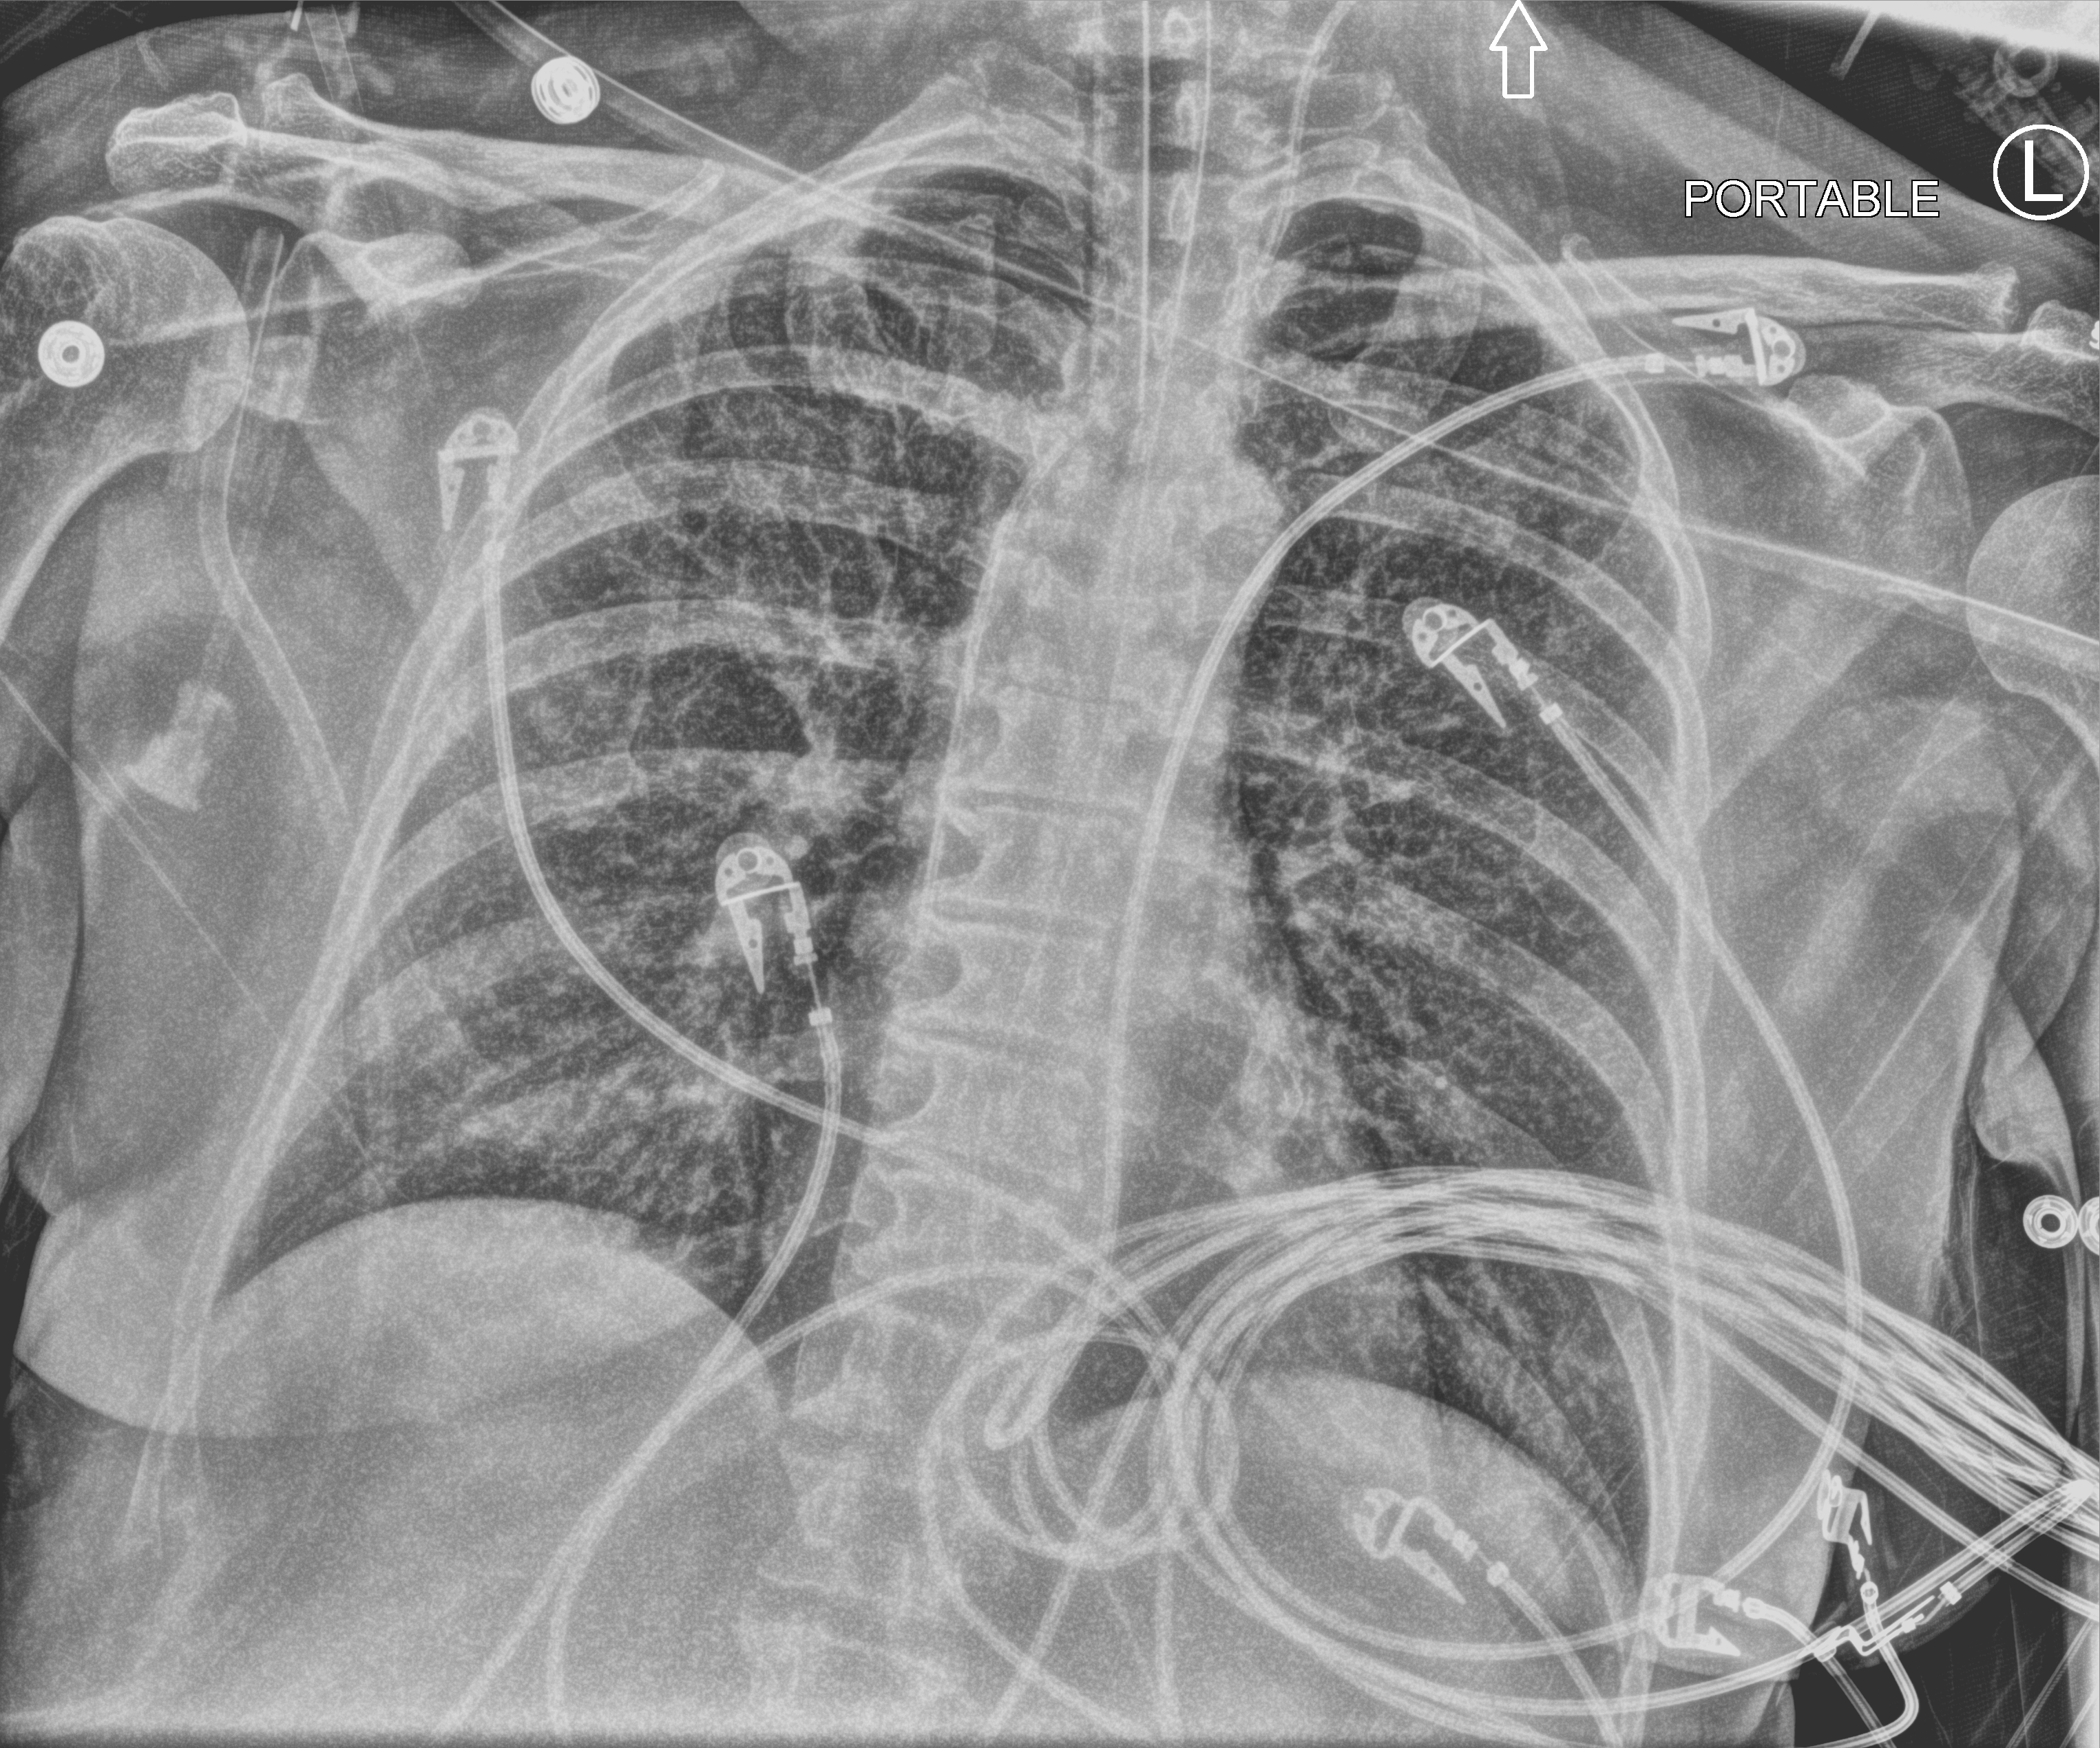
Bedside chest radiograph (computed radiography); anteroposterior (AP) projection. Female patient hospitalised with COVID-19, age 60–74 years.
From the hospital-stay record, not from the radiograph (when in the stay this image was taken is not recorded): admitted to intensive care during this hospital stay: yes; mechanically ventilated during this hospital stay: yes.